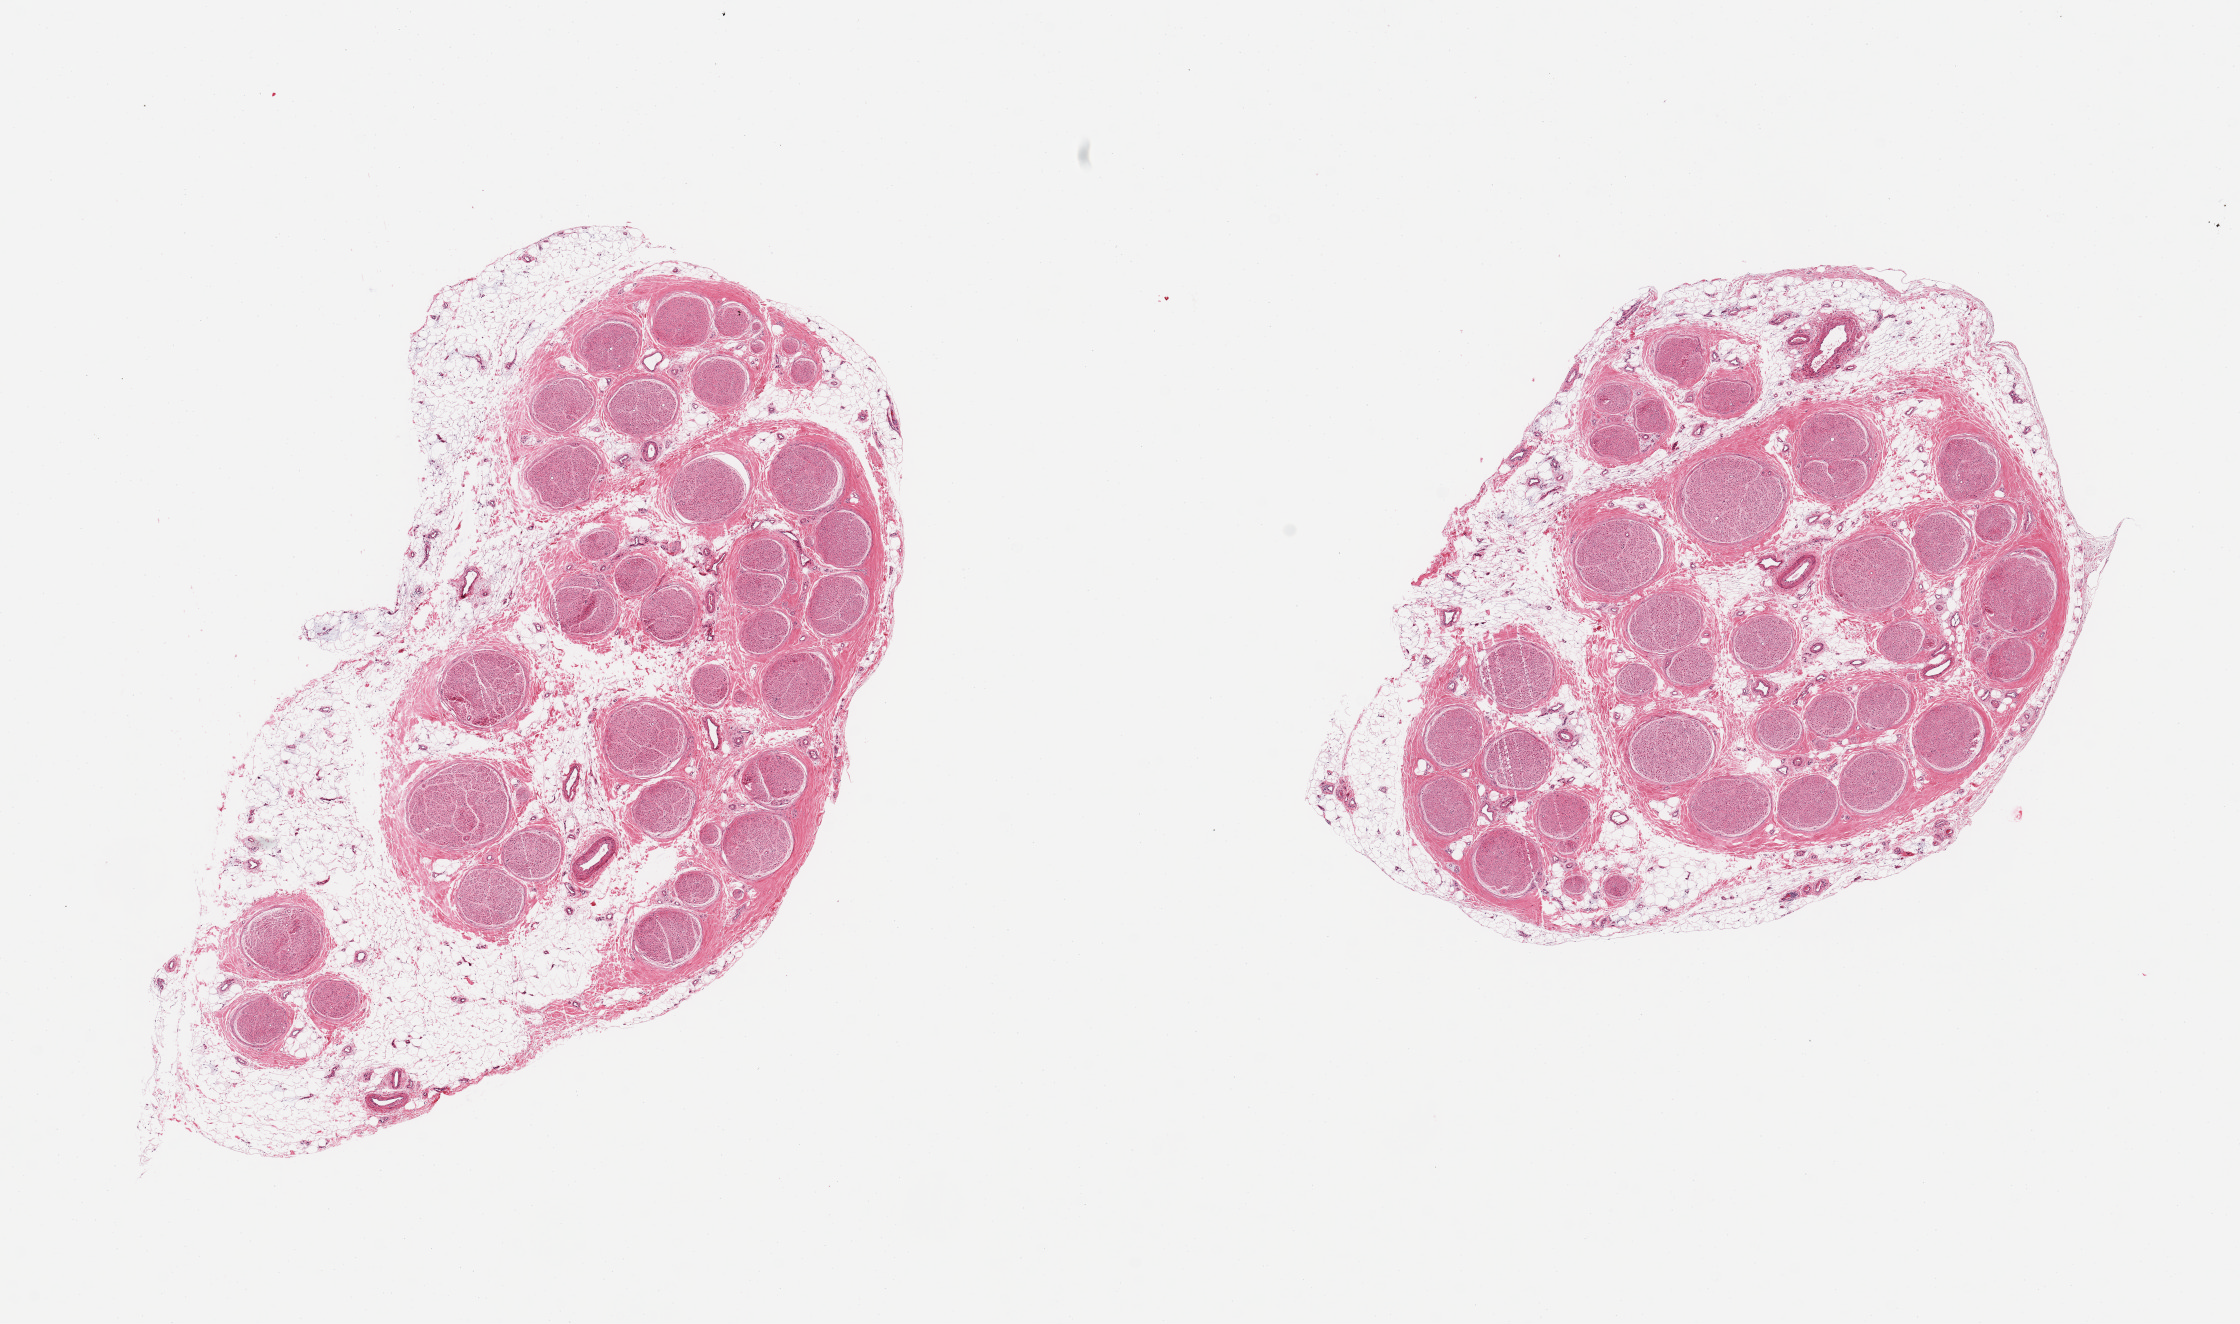
Whole-slide image, haematoxylin and eosin stain, a low-resolution overview of the entire scanned area, about 17.7 x 10.5 mm. PAXgene-fixed paraffin-embedded (PFPE) section. Target tissue: tibial nerve. Donor tissue sample. Donor: male.
Reviewer comment on this tissue sample: 2 pieces; 40% & 20% internal and external fat content.